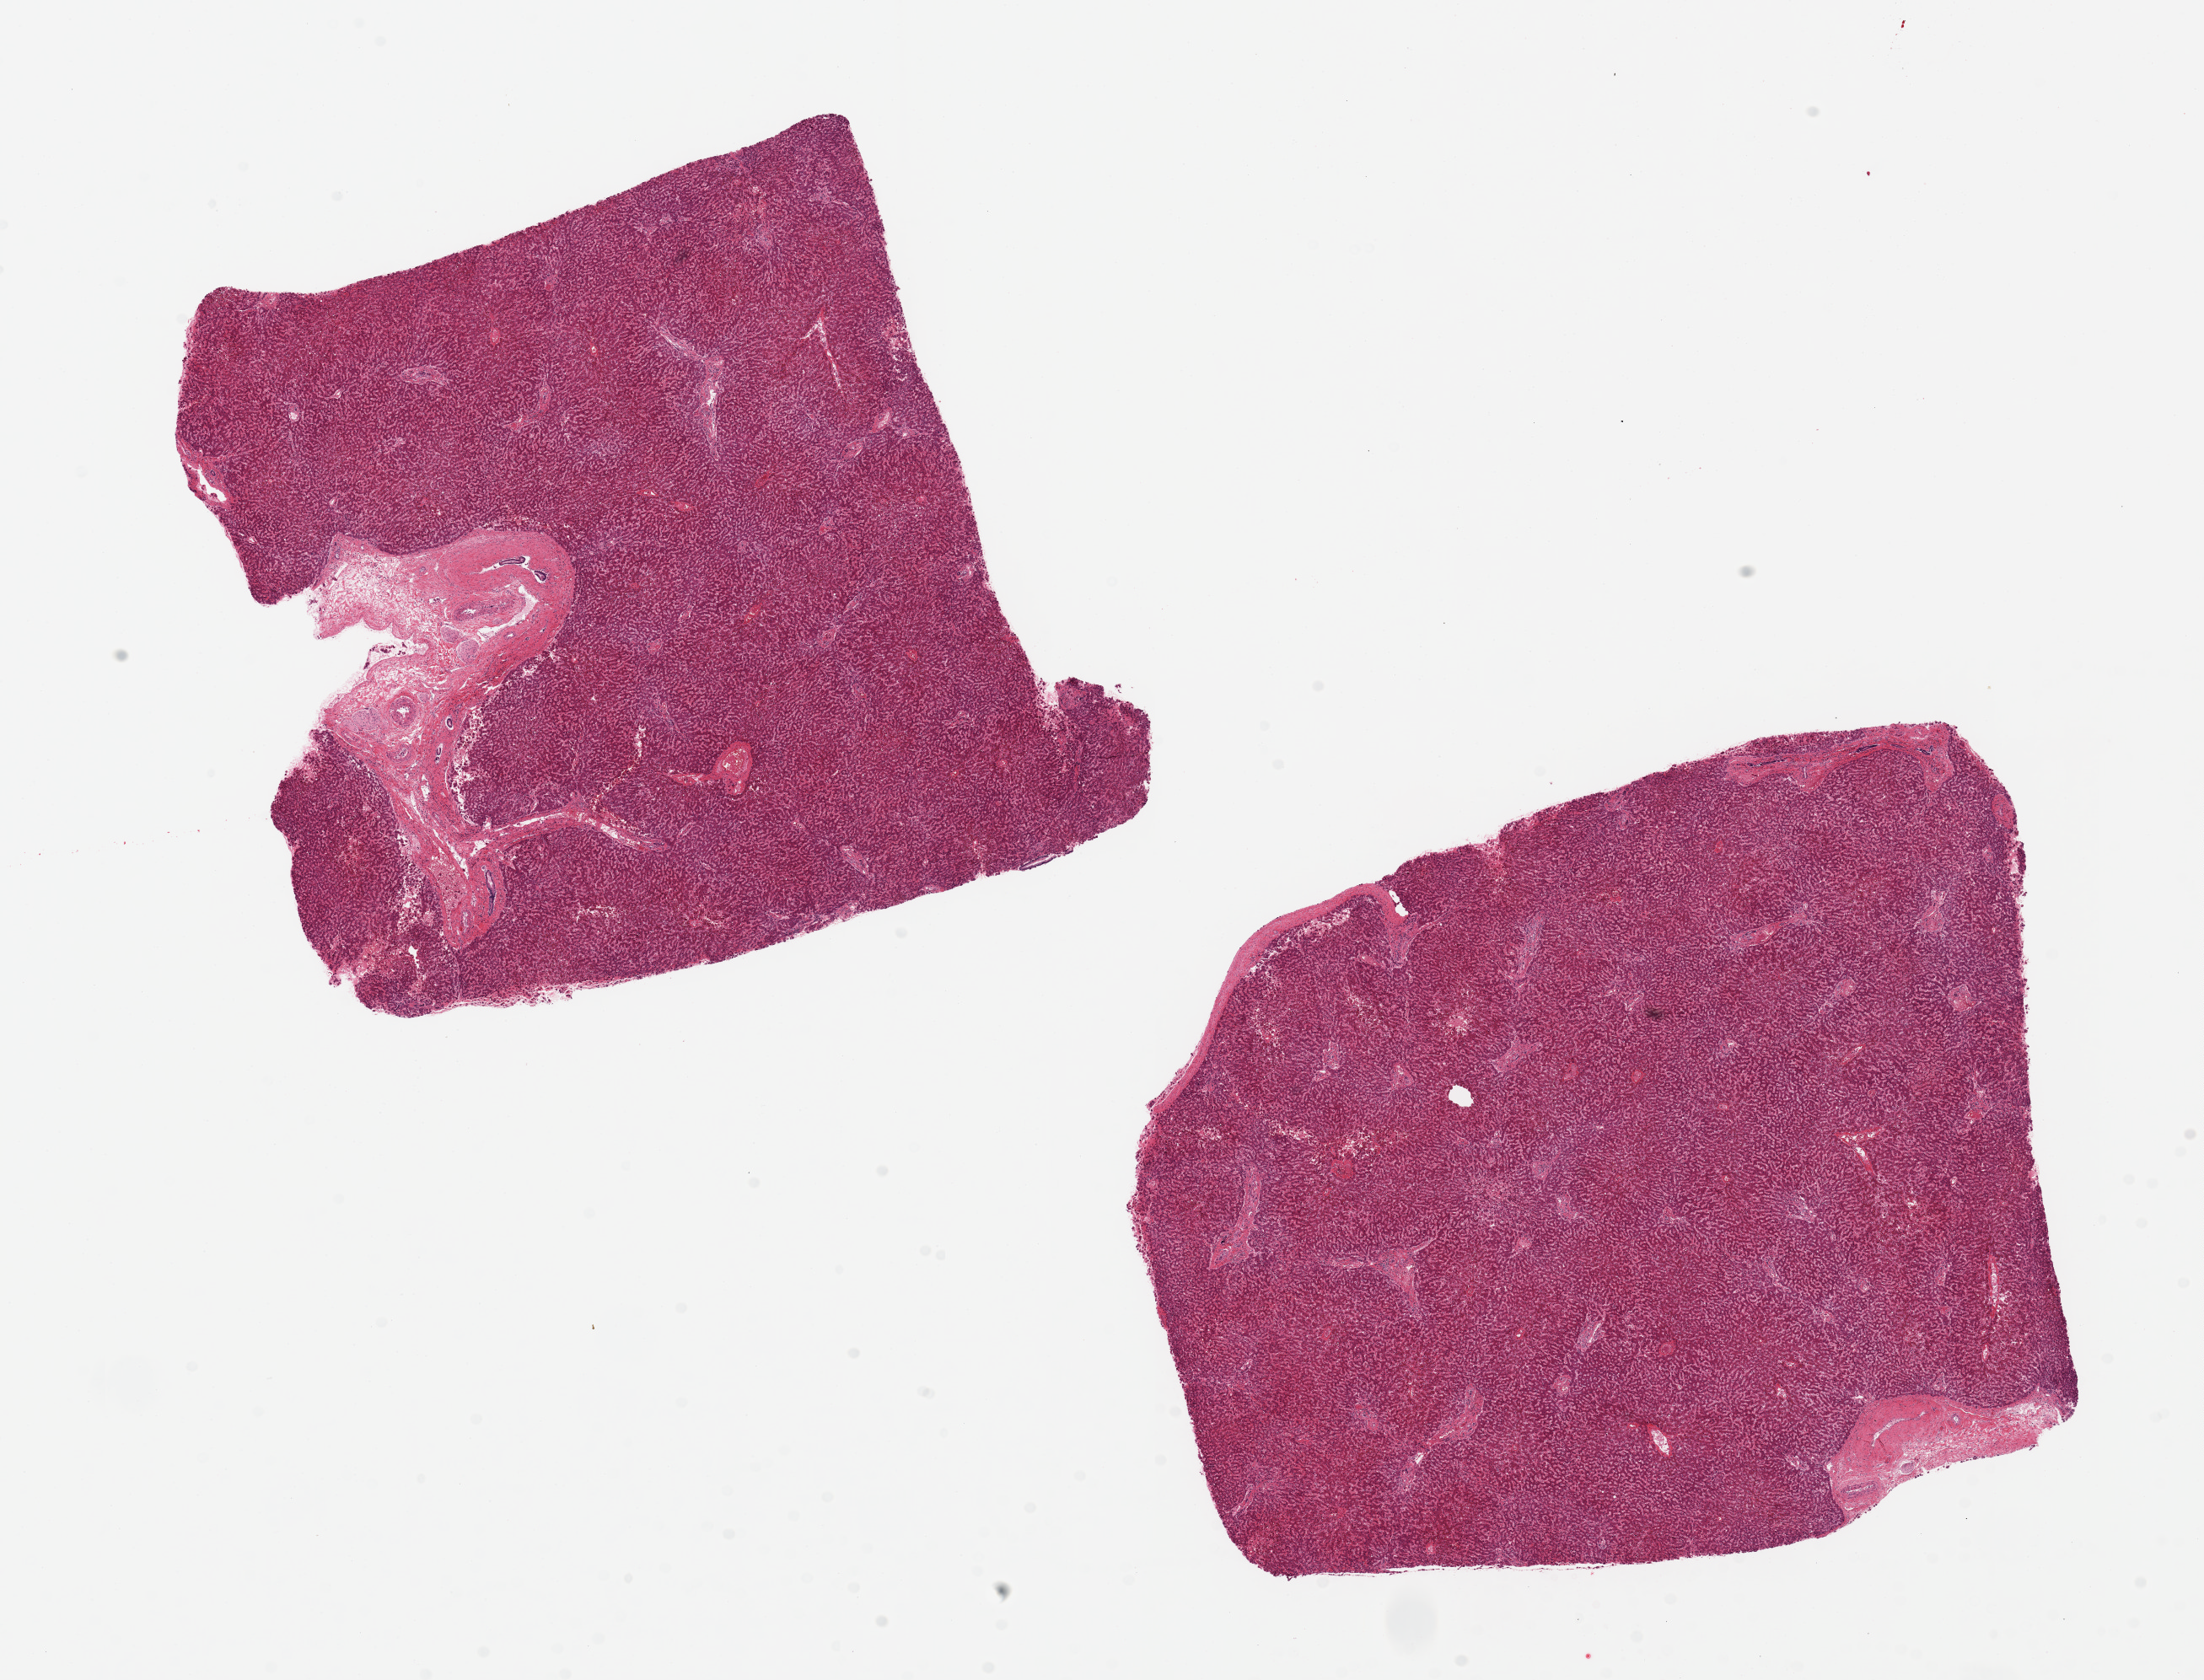
Hematoxylin and eosin (H&E) whole-slide image — a low-resolution overview of the entire scanned area, about 20.7 x 15.8 mm (acquisition: 20x scan). PAXgene-fixed, paraffin-embedded tissue. Target tissue: liver. Donor tissue sample. Donor: female.
Pathologist's review note for this sample: 2 pieces~8x7mm. Reasonably well- preserved, no steatosis noted.